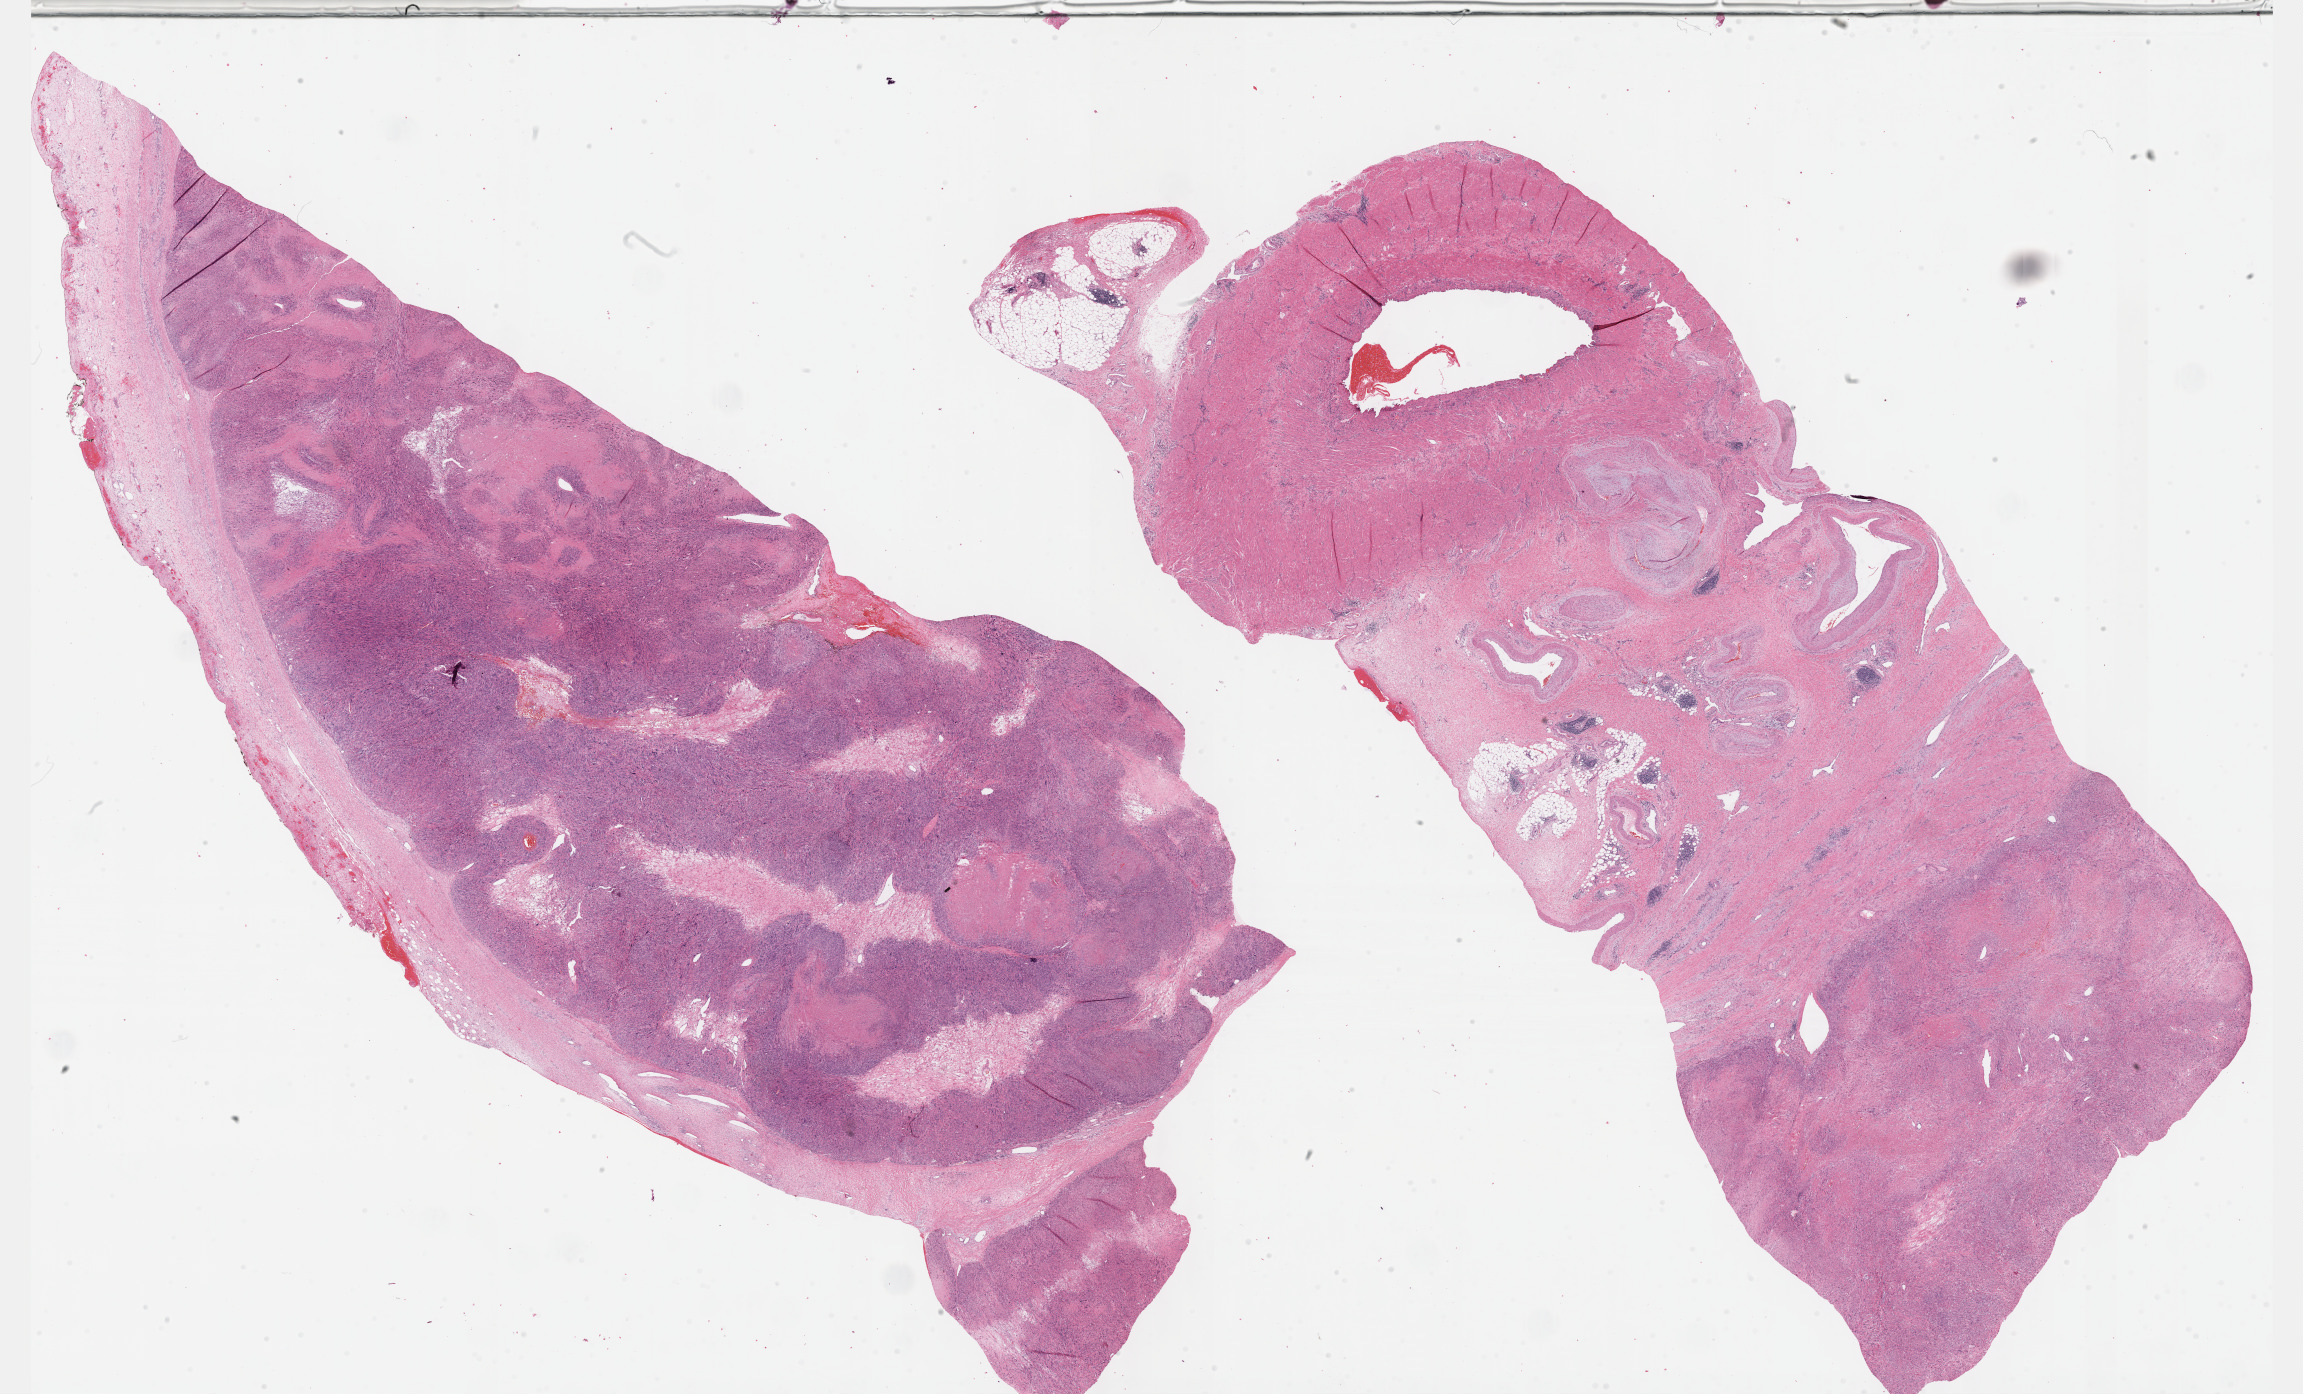
H&E-stained whole-slide image, a low-resolution overview of the entire scanned area, about 37.2 x 22.5 mm (from a 40x scan), FFPE section, retroperitoneum and peritoneum, primary tumour sample. Female patient; age at initial diagnosis 63 years.
Diagnosis: Leiomyosarcoma, NOS (retroperitoneum).